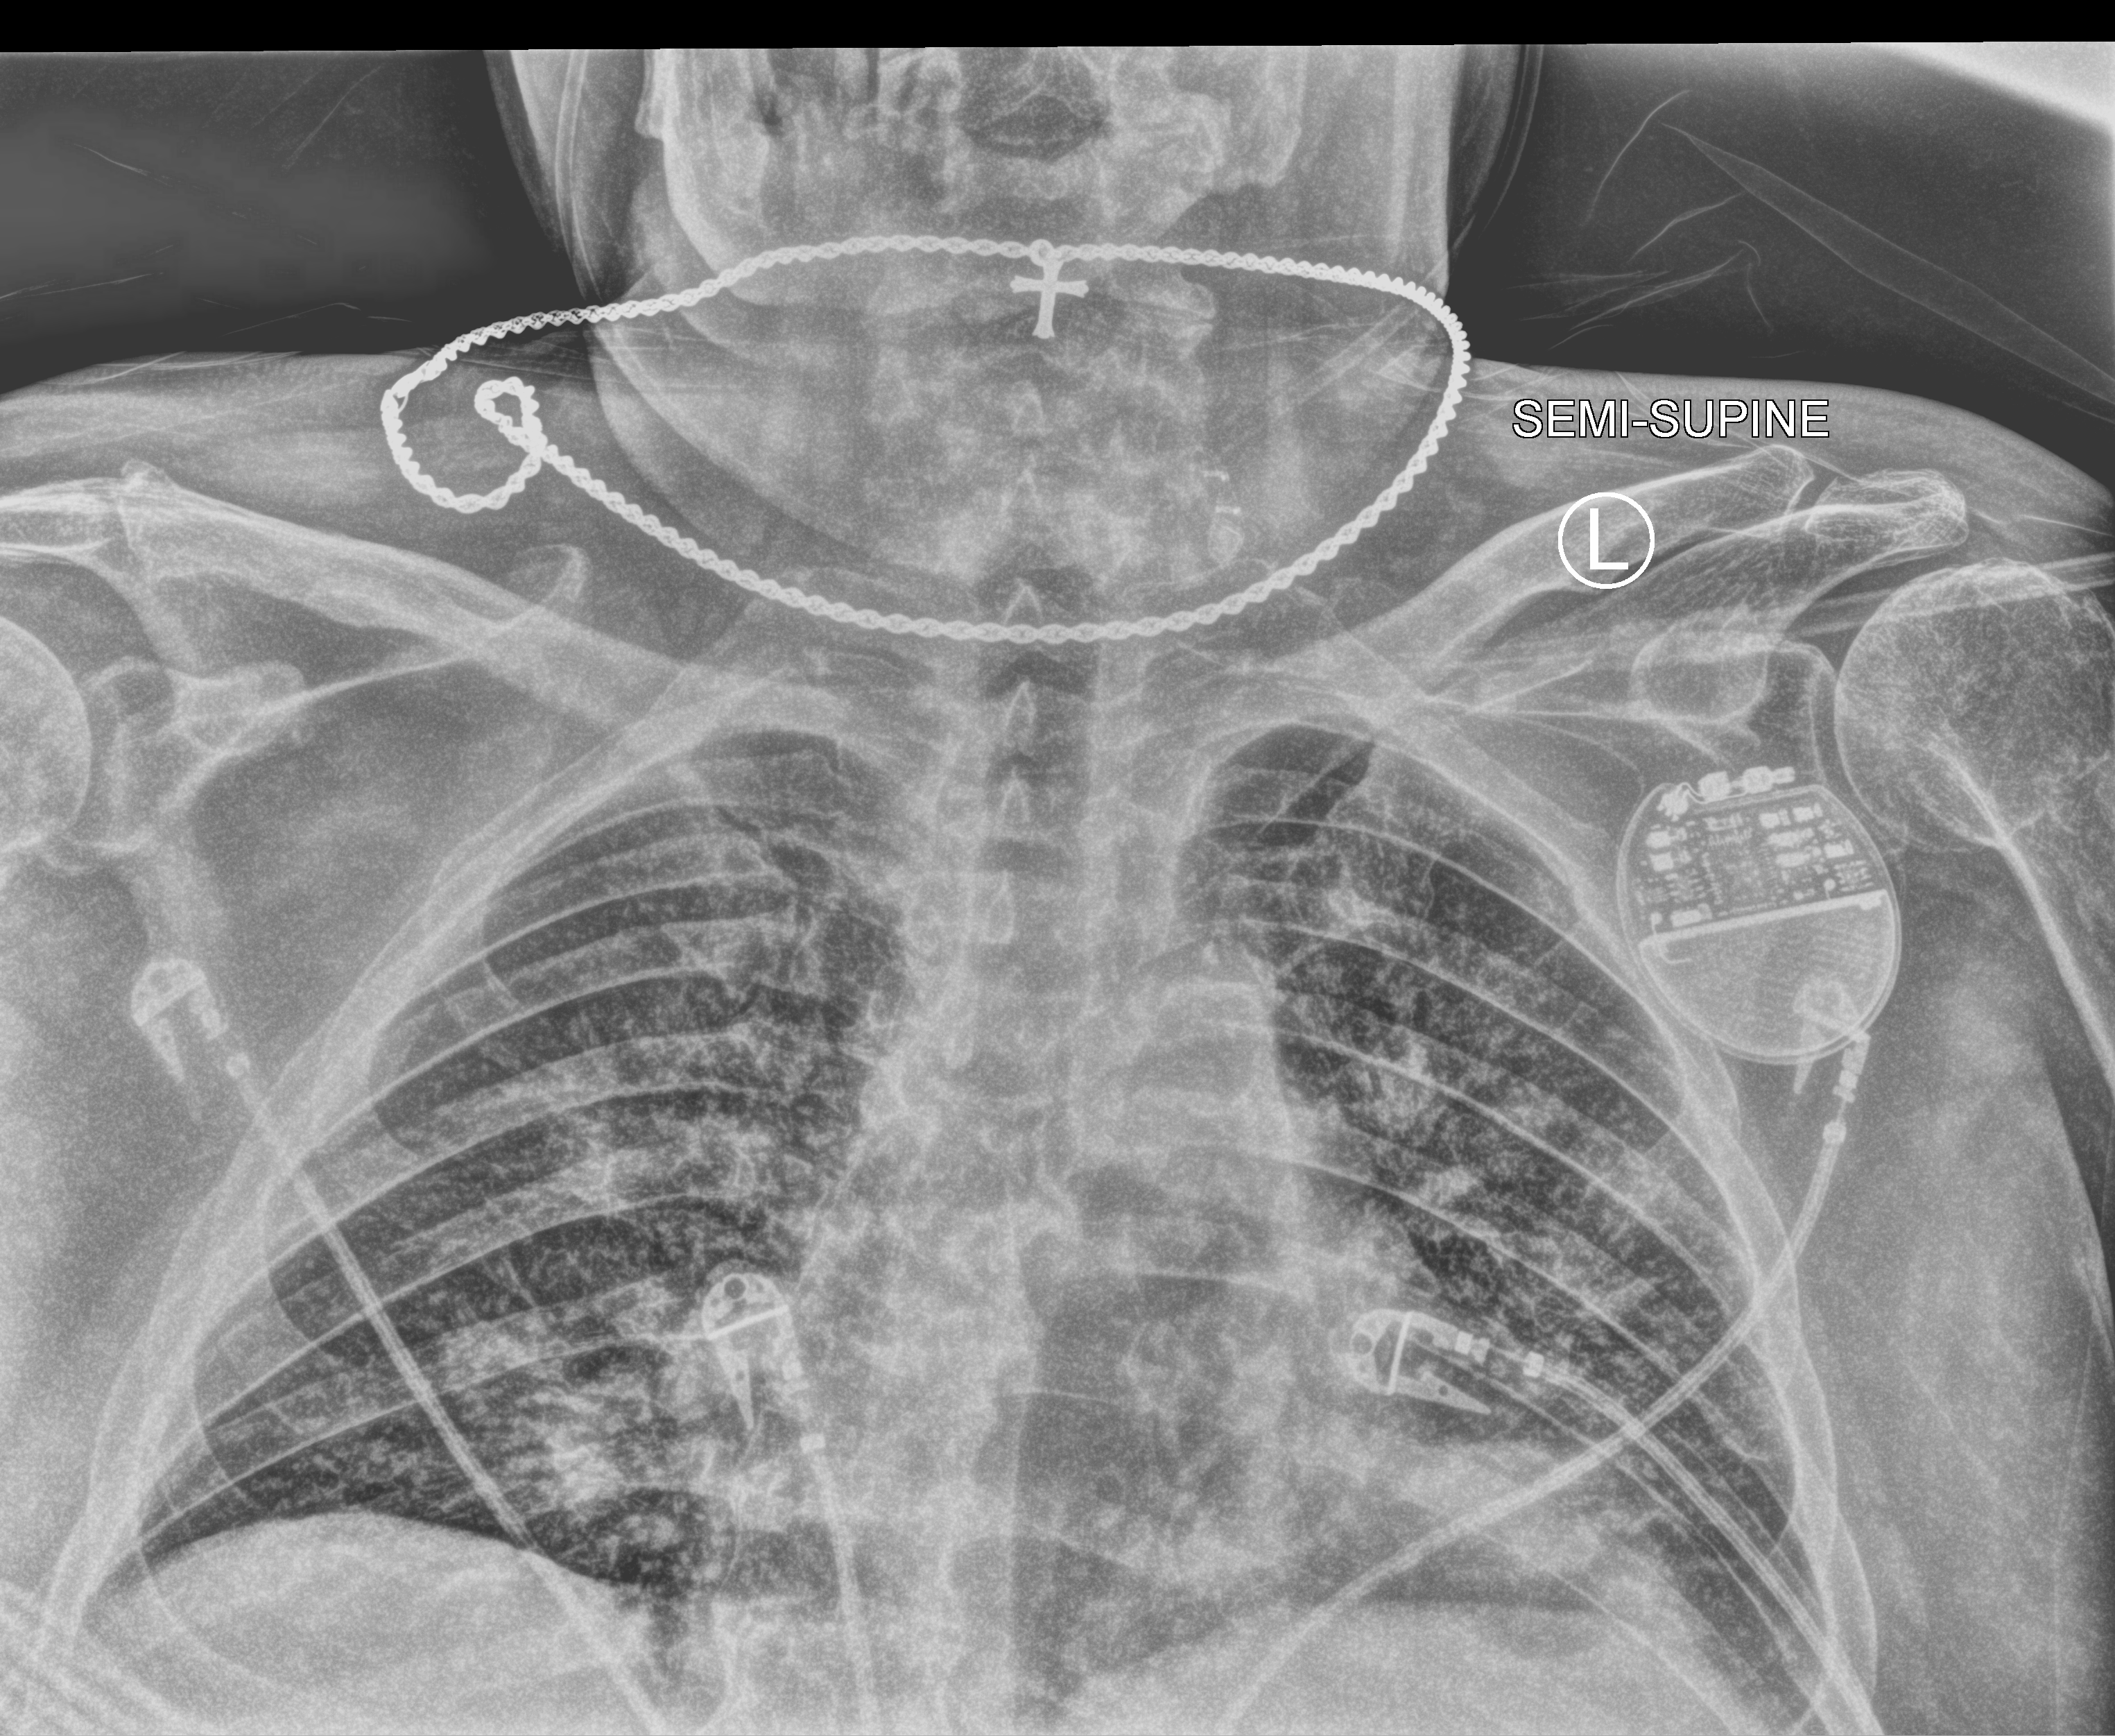
Portable chest radiograph; anteroposterior (AP) projection. Male patient hospitalised with COVID-19, age 60–74 years.
From the hospital-stay record, not from the radiograph (when in the stay this image was taken is not recorded): hypertension (admission record): yes; admitted to intensive care during this hospital stay: no; mechanically ventilated during this hospital stay: no.